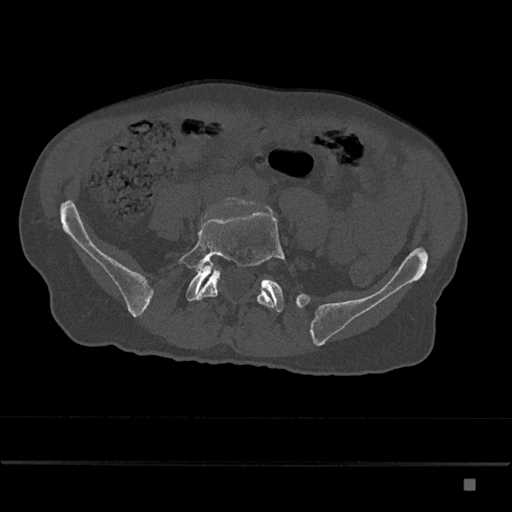
CT including the spine, one axial slice. Position 270 of 797 along the scan axis. Reconstruction kernel Br40s/3. 120 kVp. Bone window (W 1800 / L 400 HU). 0.5 mm slice thickness. 512 × 512 image matrix, field of view 390 × 390 mm. Male patient, age 72 years. Case-level facts recorded for this patient, not image findings: primary cancer: prostate.
Outlined on this slice (semi-automatically segmented with operator editing):
- L5 vertebra: bounding box [x1, y1, x2, y2] px = [178, 212, 286, 308]